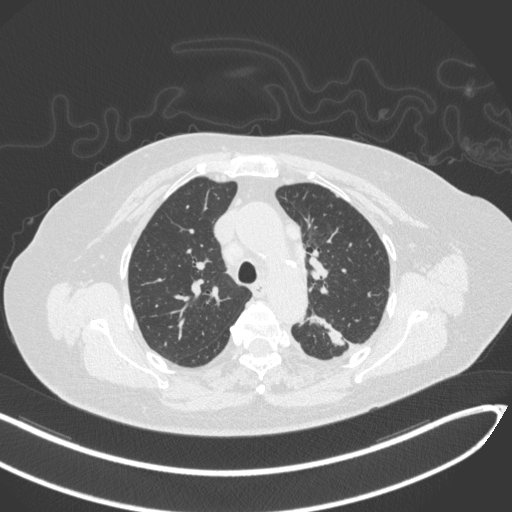
Chest CT, one axial slice. Slice 224 of 270 in the series (ordered by position). 120 kVp. Lung window (W 1500 / L -600 HU). 512 × 512 image matrix, field of view 400 × 400 mm. Female patient, age 76 years. From the clinical record (not read from this slice): clinical TNM (as recorded): T1c N0 M0.
Structures marked on this image (rectangle marked by the reading radiologist):
- lung tumour (recorded histology: adenocarcinoma): bounding box [x1, y1, x2, y2] px = [307, 306, 352, 353]